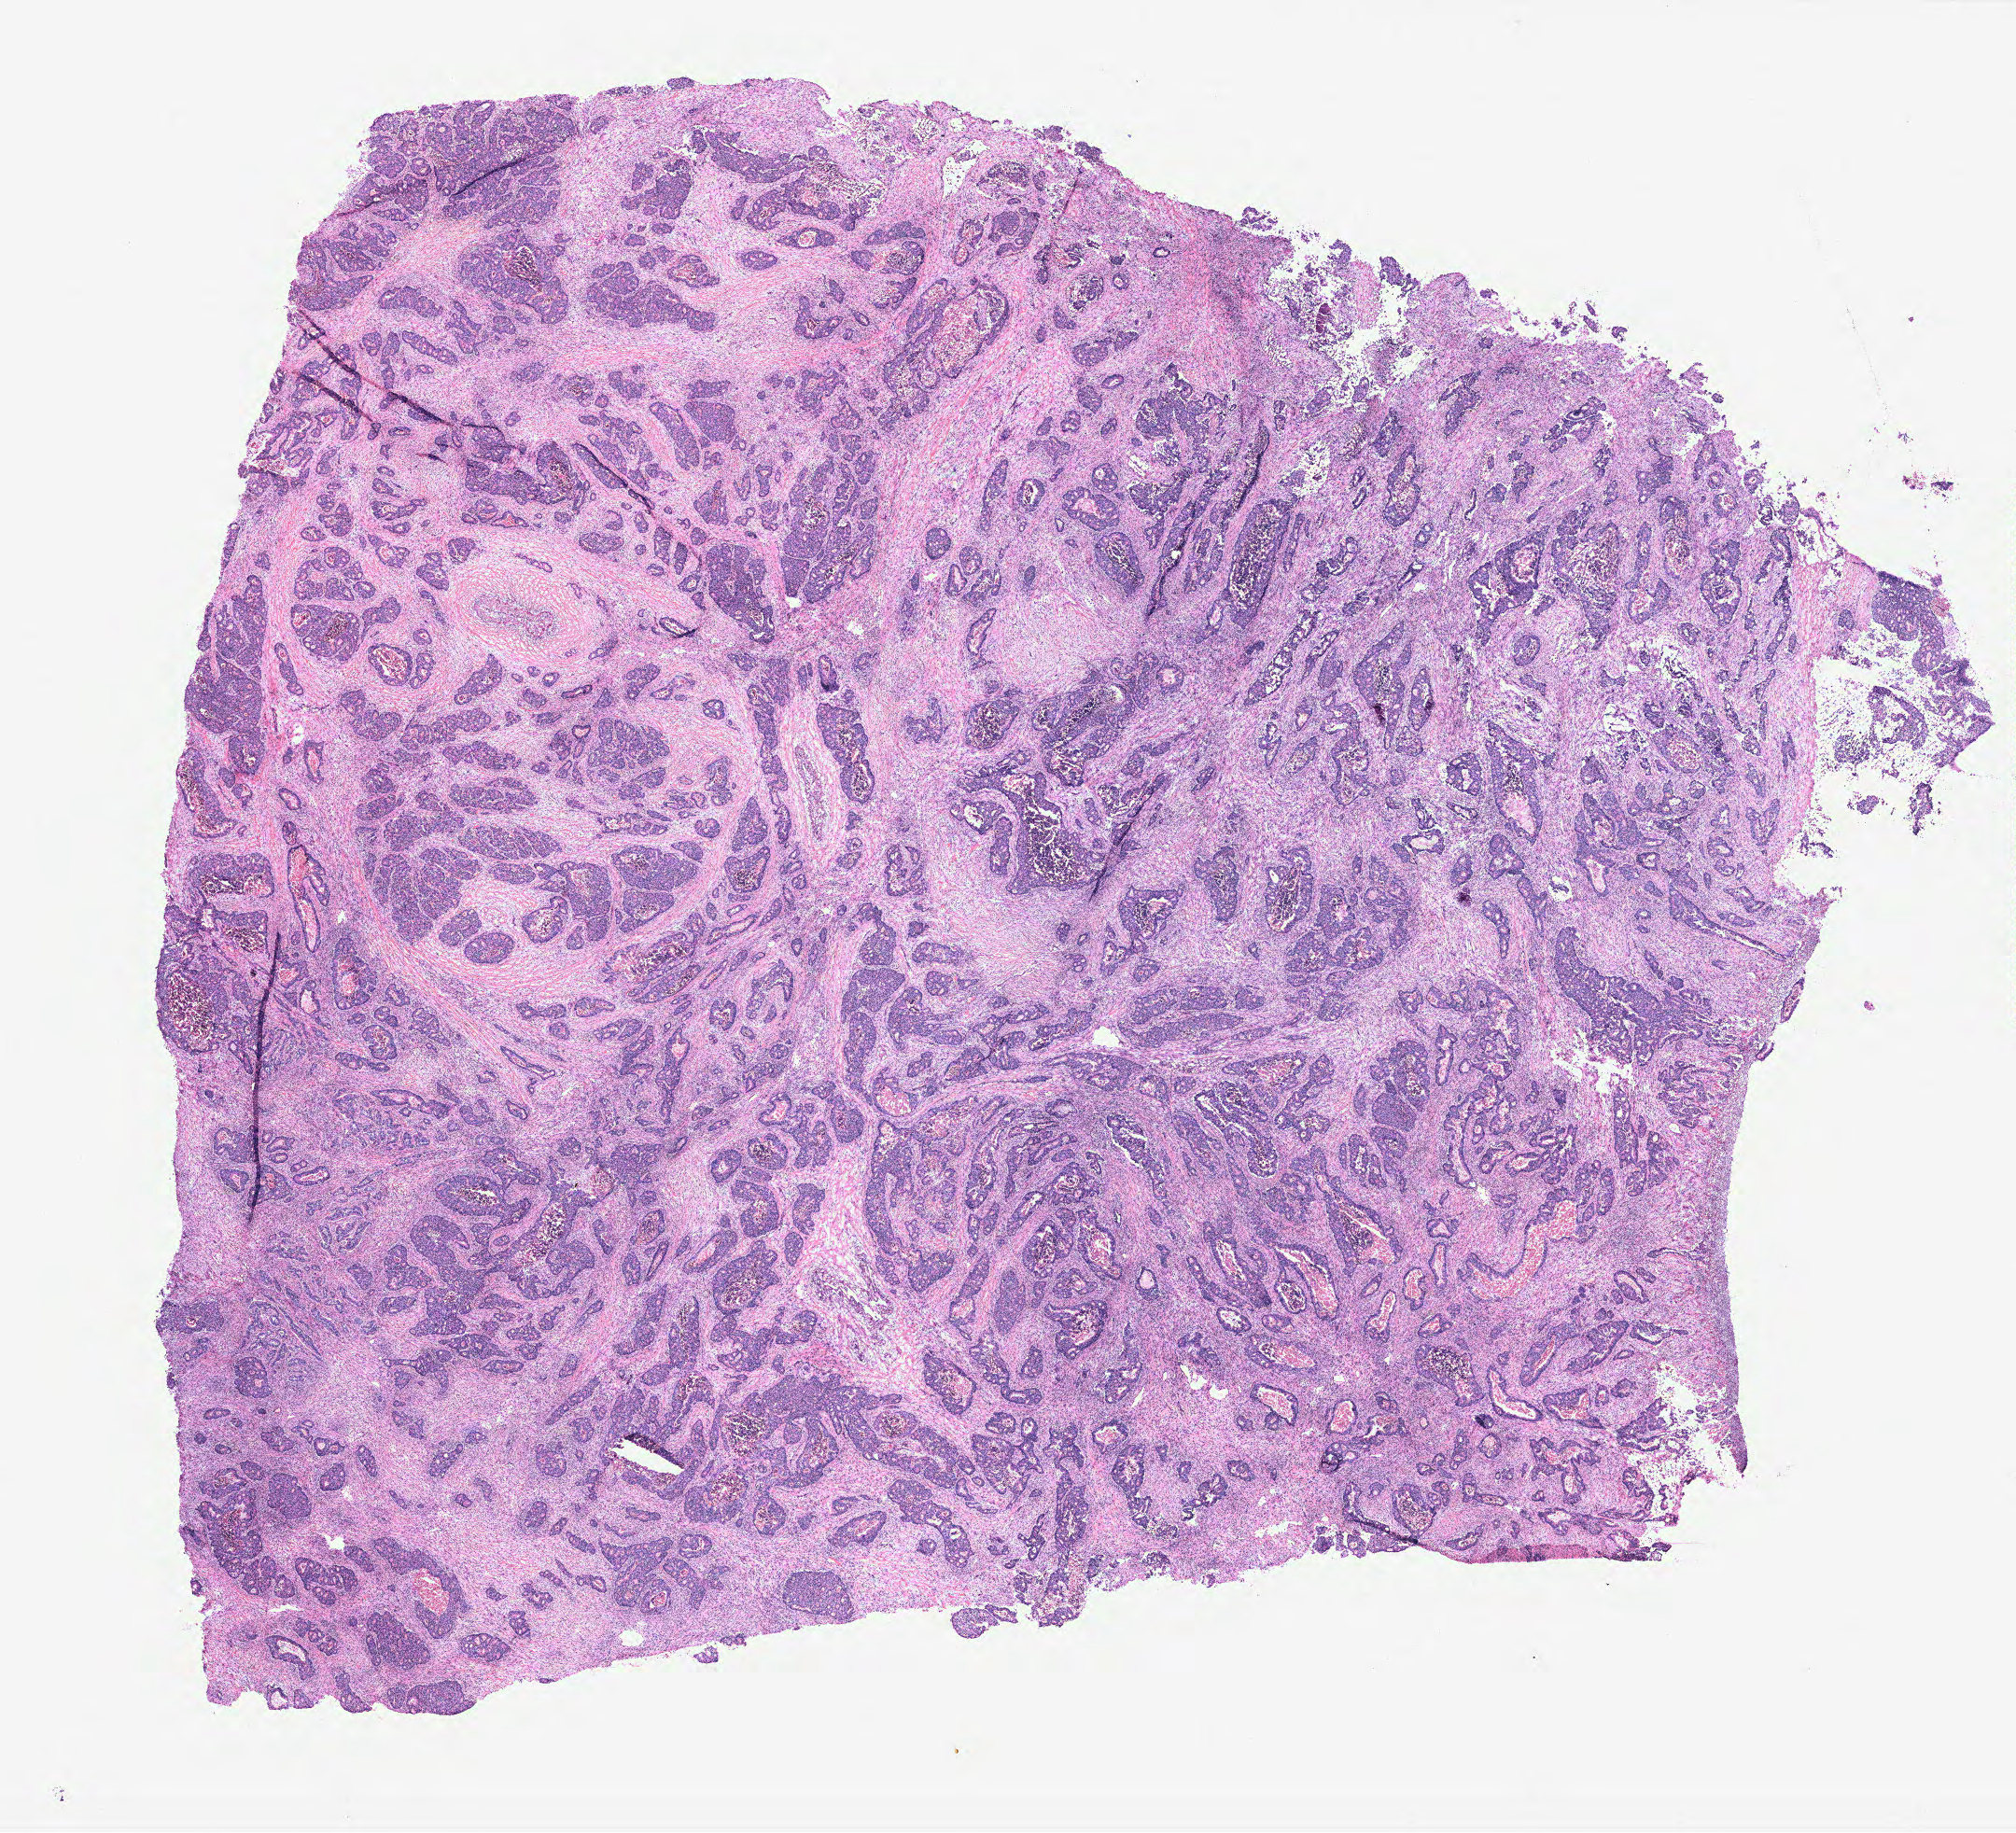
Digitized H&E tissue section (whole slide) — whole scanned area (about 17.3 x 15.7 mm, from a 40x scan) shown as a low-resolution overview; colon, normal (non-tumour) tissue. 64-year-old female patient.
- this section: normal (non-tumour) tissue from the same patient
- patient diagnosis: Adenocarcinoma, NOS